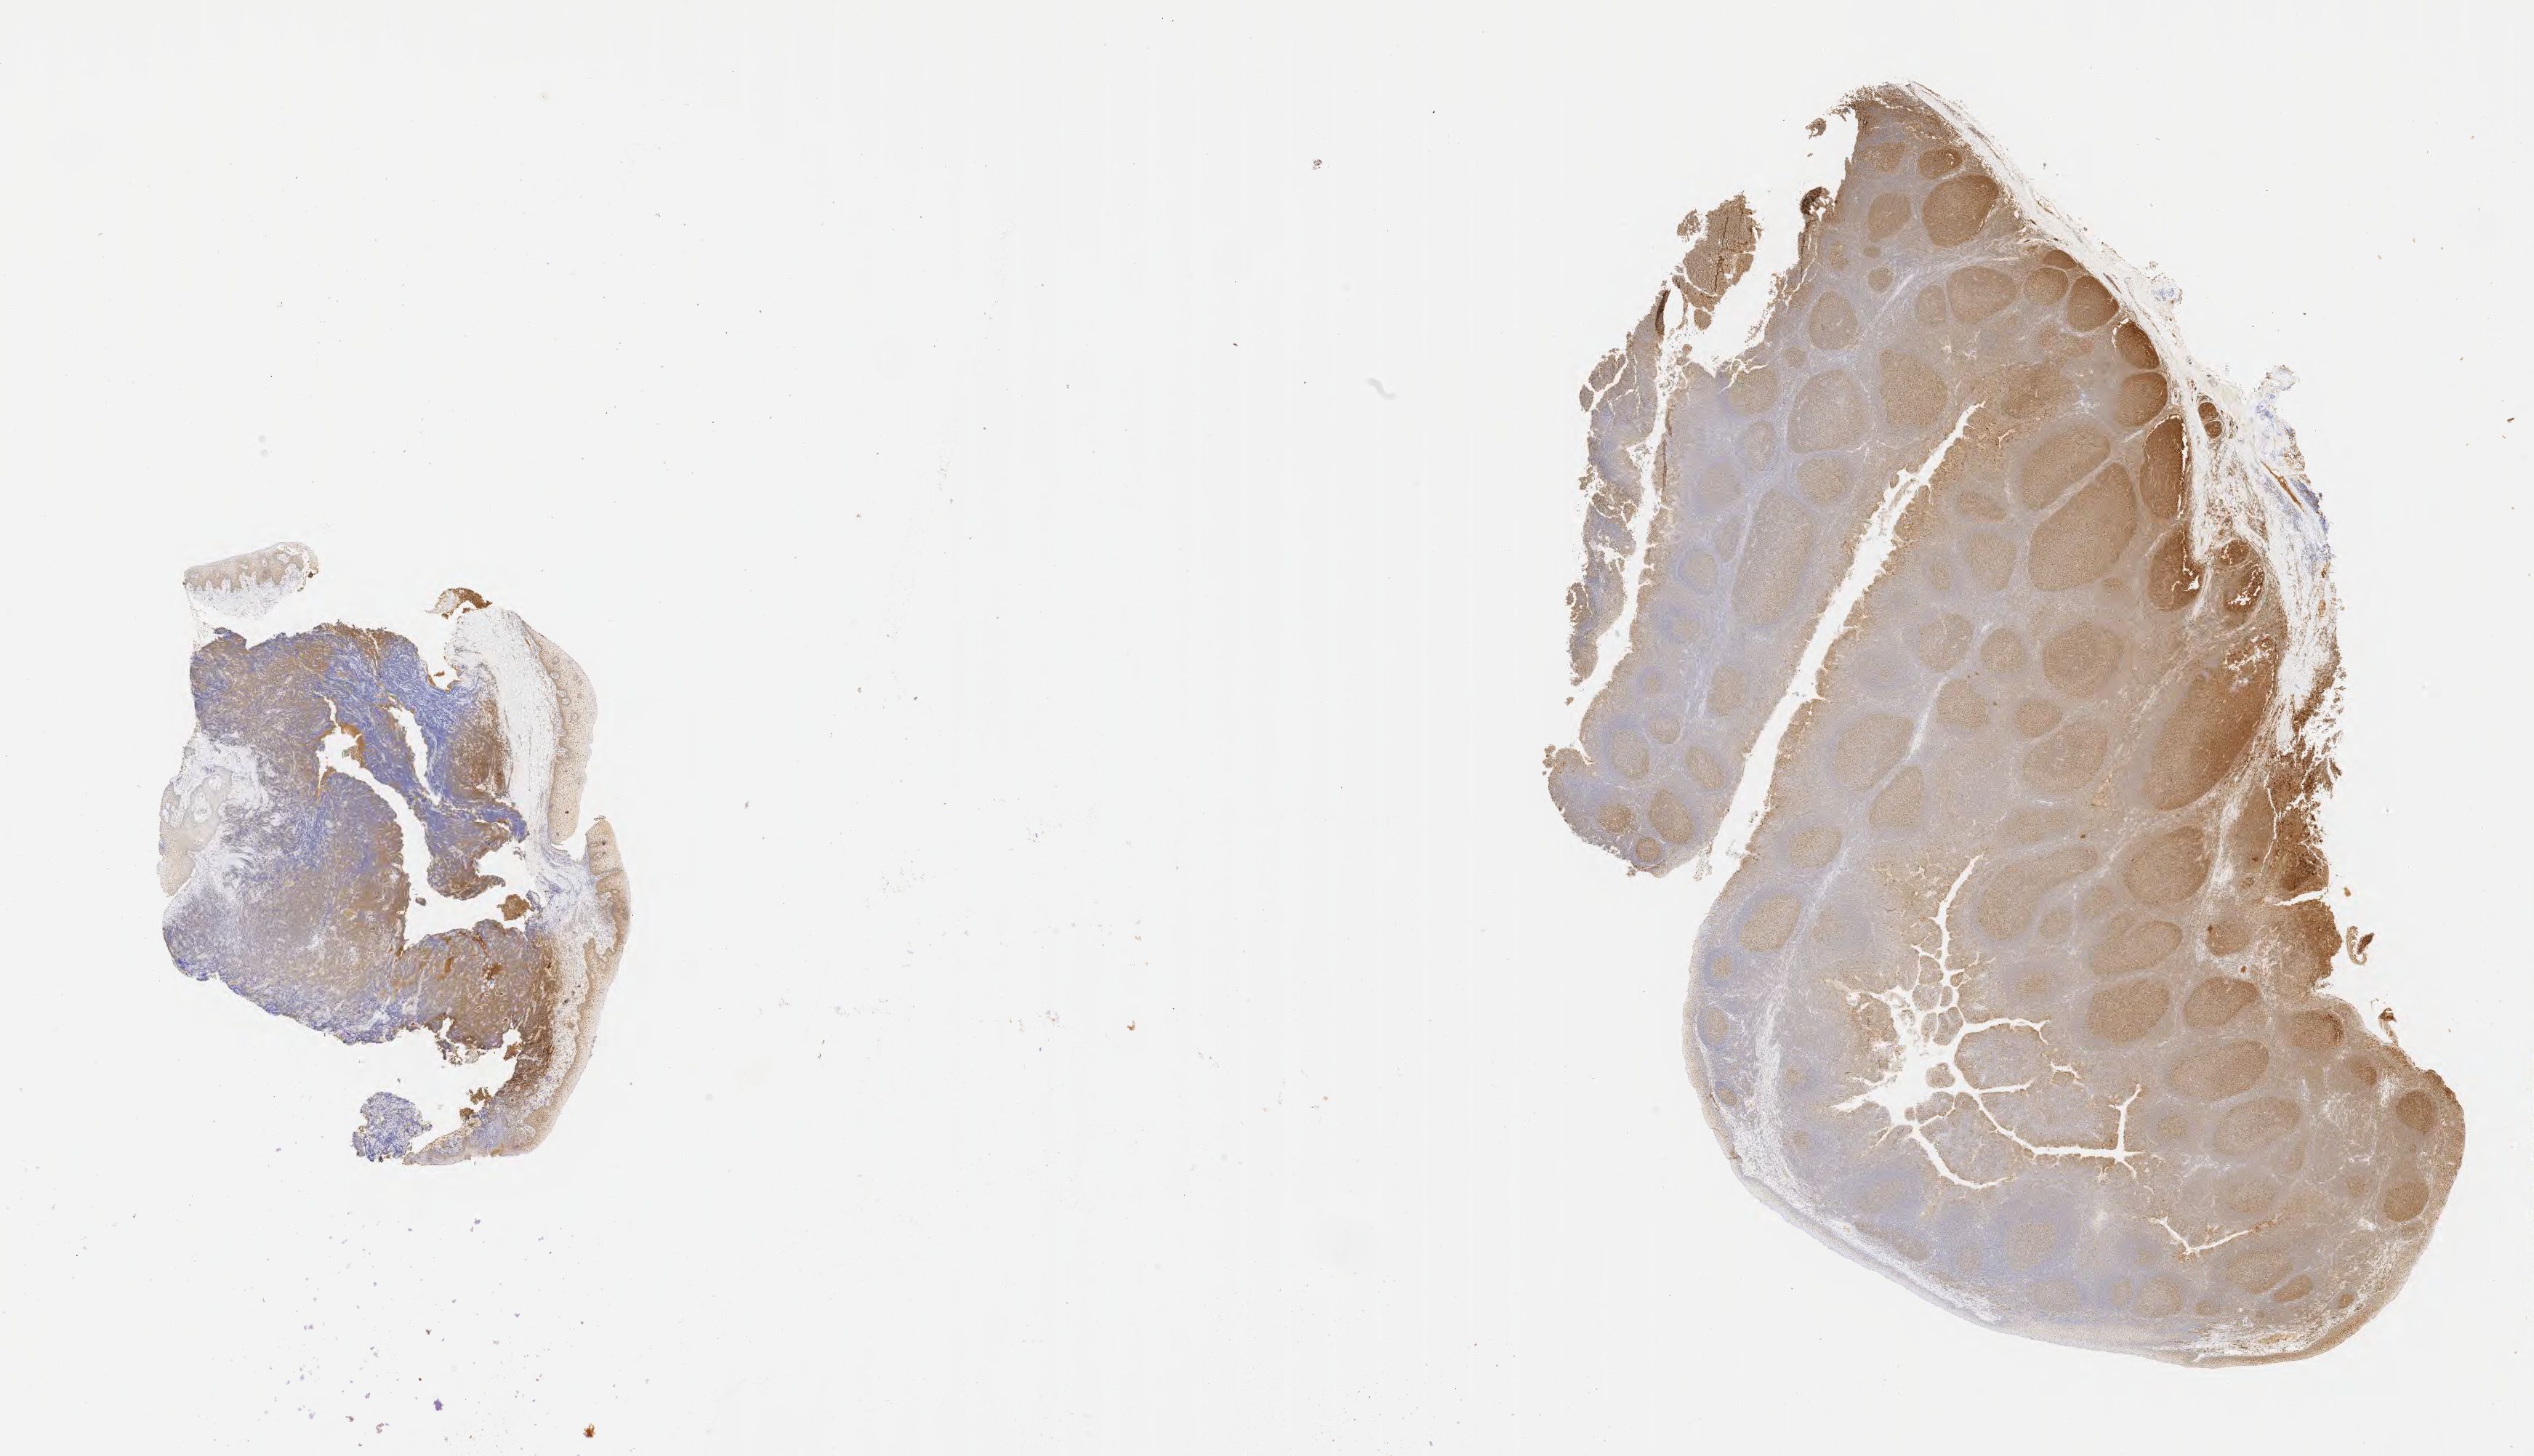
Immunohistochemistry (IHC) whole-slide image stained for BCL6 — a low-resolution overview of the entire scanned area, about 28.2 x 16.2 mm, specimen: tumor tissue, site: mandible. Female patient; age at initial diagnosis 7 years.
* diagnosis: Burkitt lymphoma, NOS